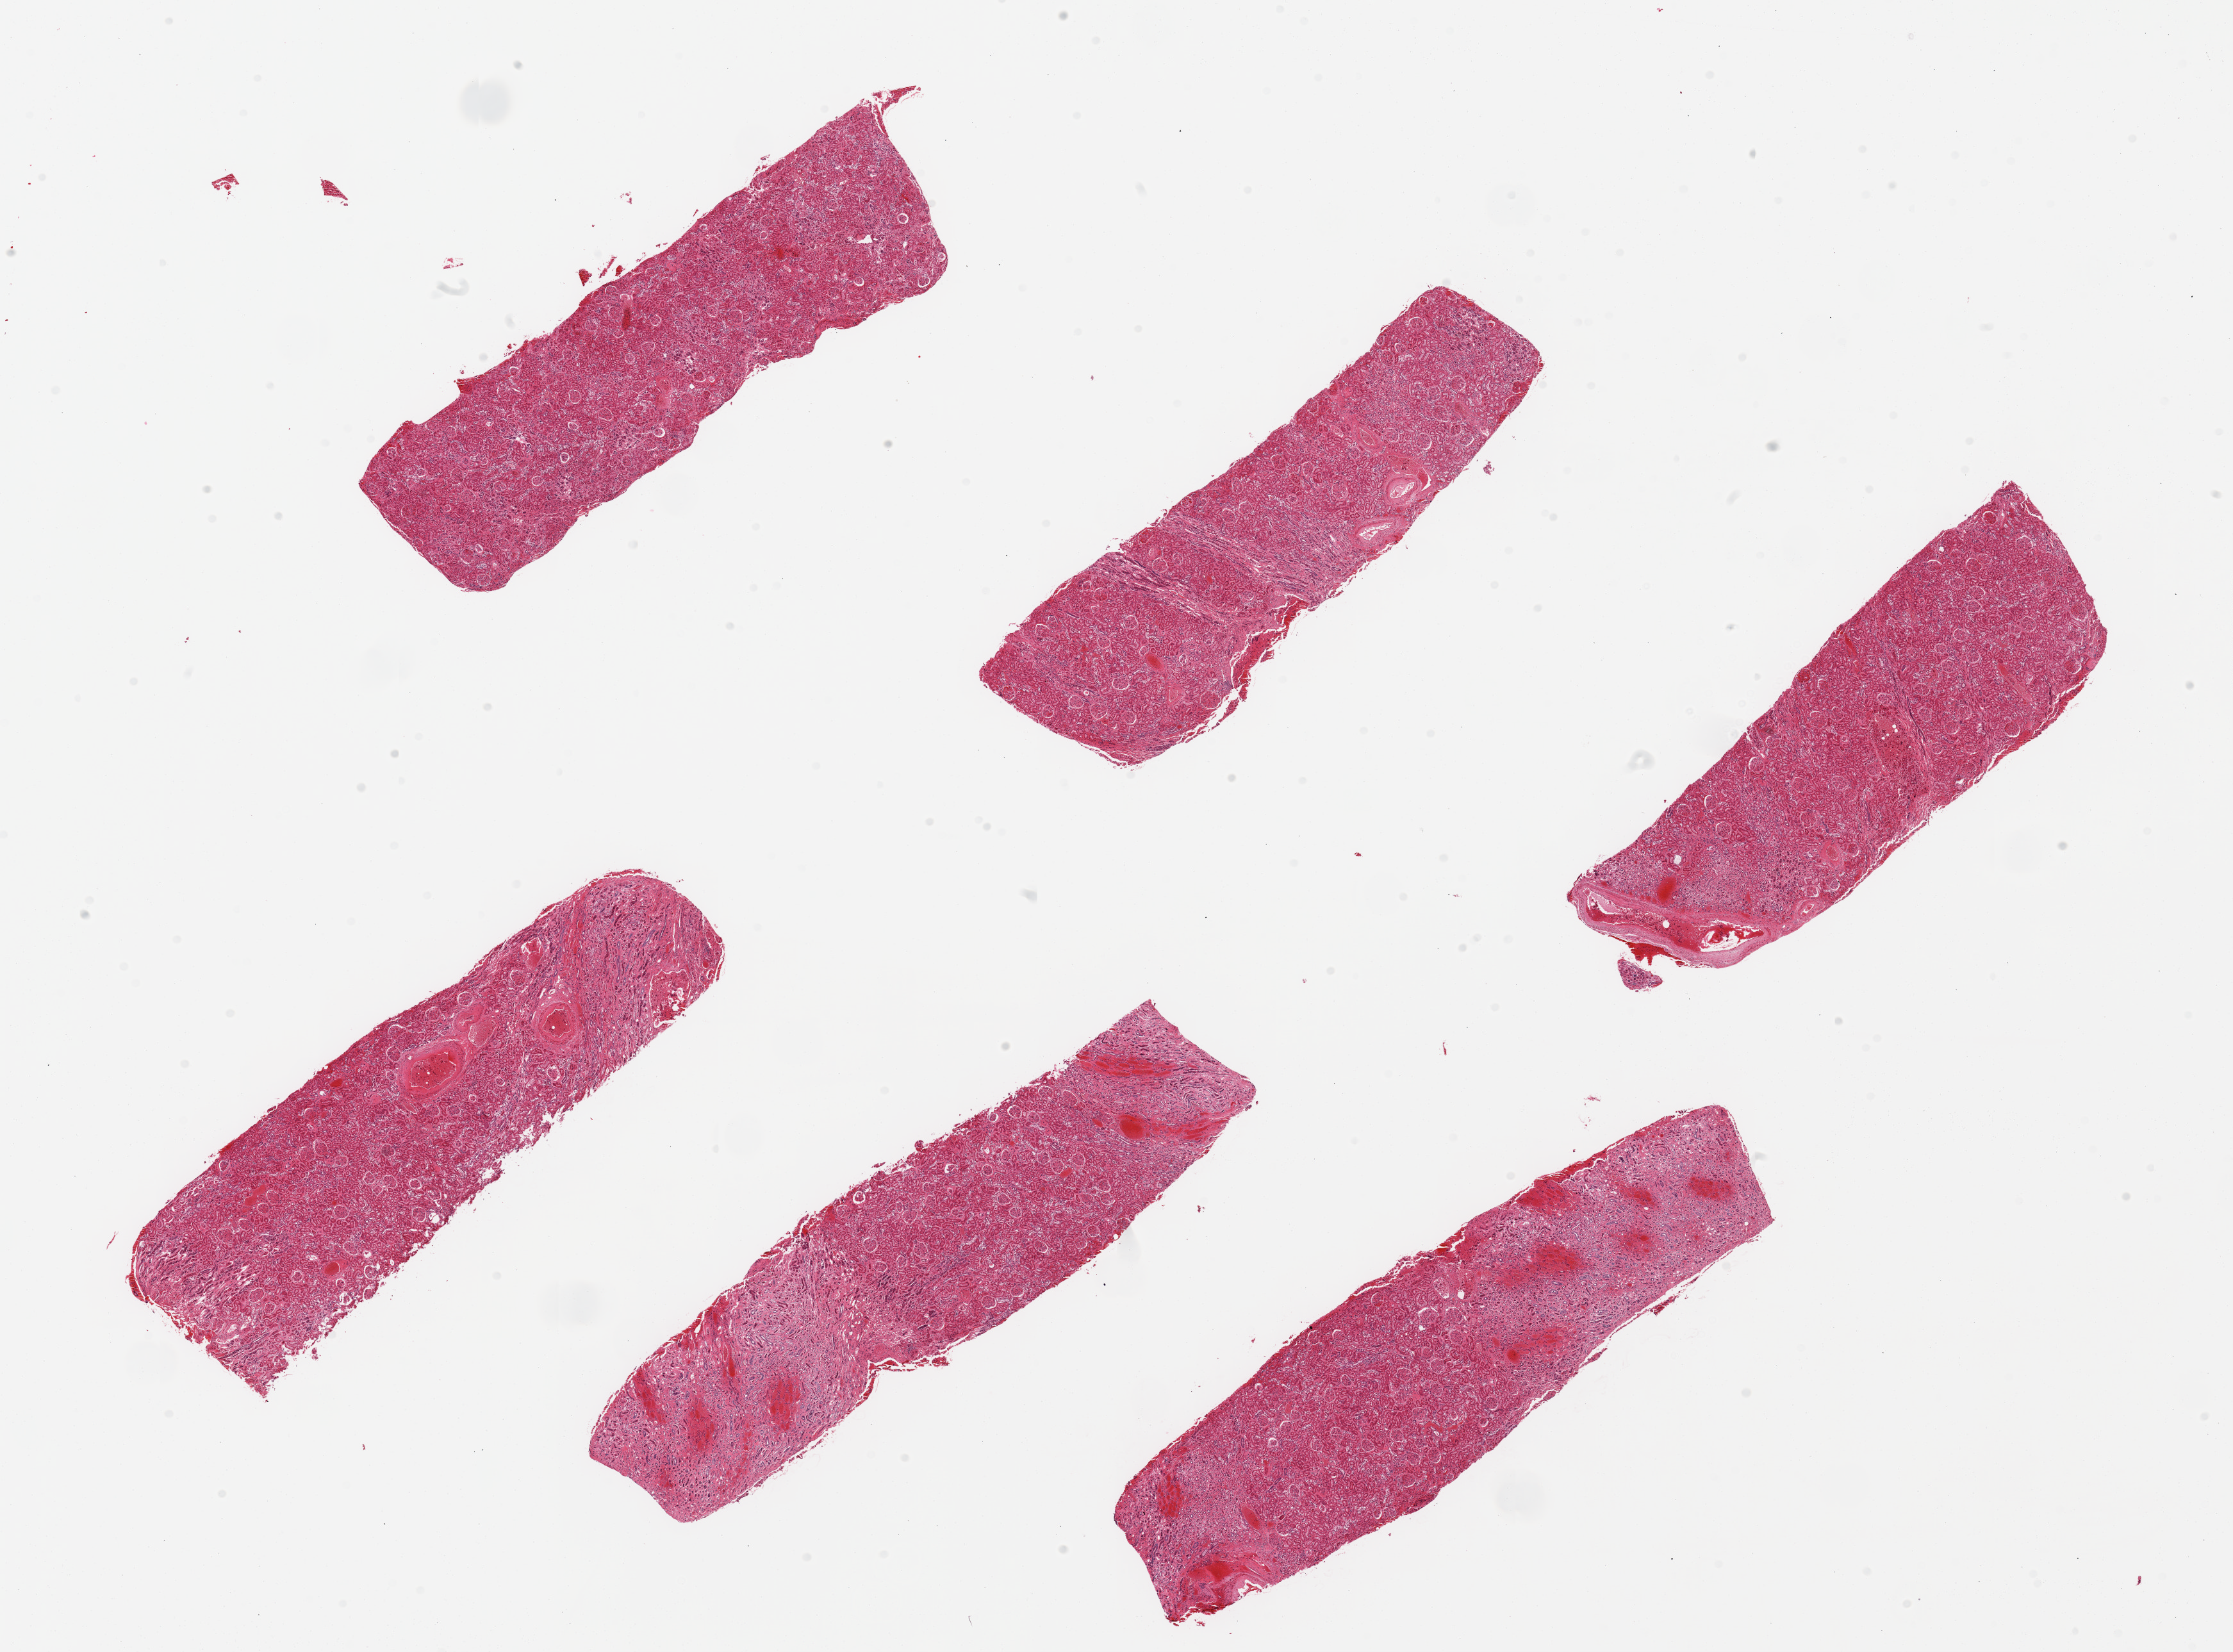
Hematoxylin and eosin (H&E) whole-slide image, shown as a low-resolution overview of the whole scanned area (about 27.6 x 20.4 mm); PAXgene-fixed paraffin-embedded (PFPE) section; sampled site (target tissue): renal cortex; tissue donor sample.
• pathologist's review note for this sample: 6 pieces; multiple pieces contain medulla (up to 40%); congestion